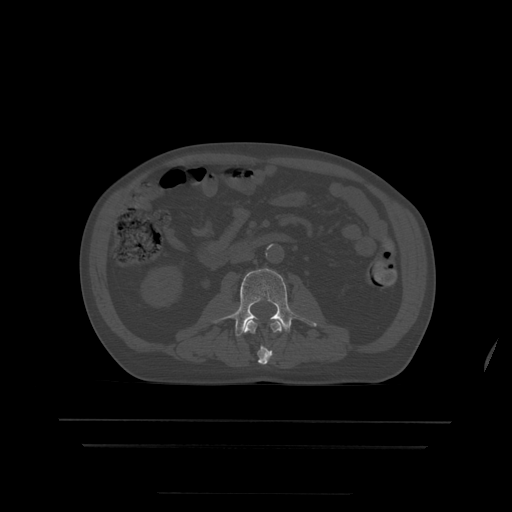
CT including the spine, one axial slice. Bone window (W 1800 / L 400 HU). 1.25 mm slice thickness. 512 × 512 image matrix, field of view 436 × 436 mm. Patient age 68 years. Case-level facts recorded for this patient, not image findings: primary cancer: urothelial.
Annotated regions visible in this slice (semi-automatic segmentation, software-assisted and operator-edited):
- L2 vertebra: bounding box [x1, y1, x2, y2] px = [245, 321, 282, 365]
- L3 vertebra: [214, 269, 317, 337]